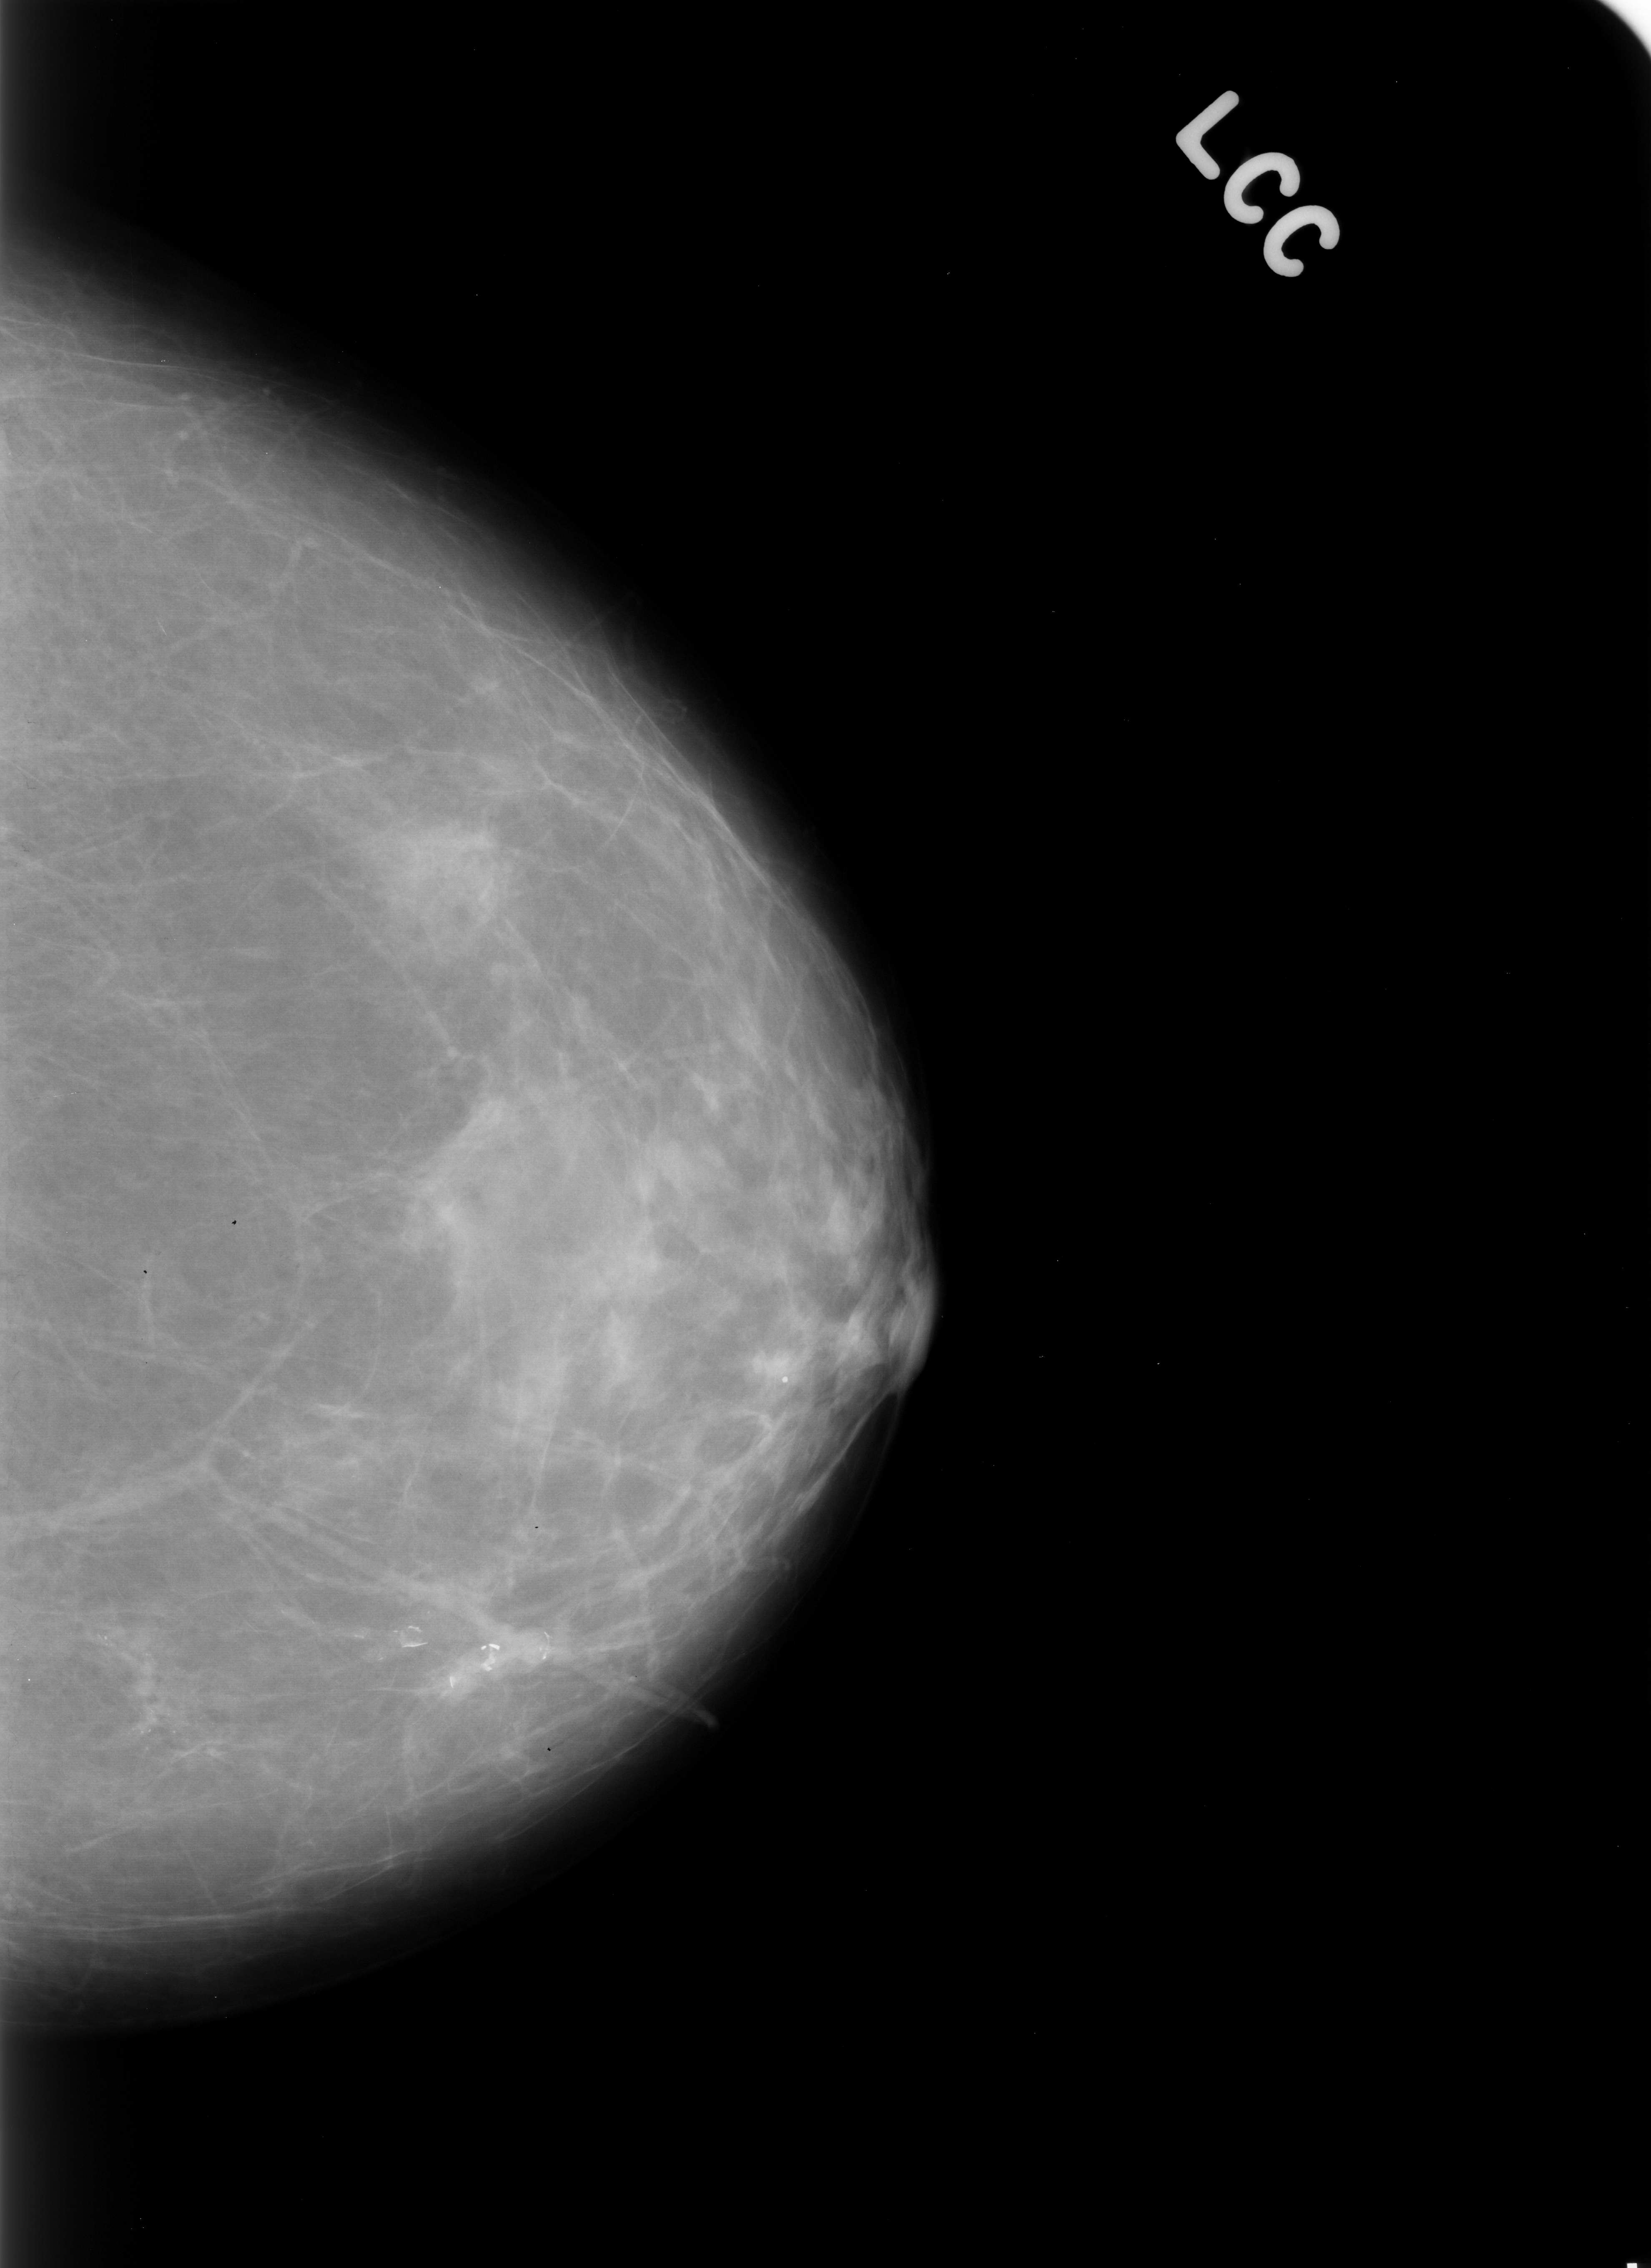
Scanned film-screen mammogram. Left breast. CC view. BI-RADS breast density category 2 (scale 1–4). 1651 × 2268 image matrix.
Expert-marked regions of interest on this film, with their recorded descriptors:
- Finding 1 of 2: calcifications, morphology pleomorphic, distribution clustered; BI-RADS assessment category 4; pathology result (as recorded, not read from the image): malignant: box from (x=33, y=1550) to (x=241, y=1815) px
- Finding 2 of 2: calcifications, morphology eggshell, distribution segmental; BI-RADS assessment category 2; outcome (as recorded, no biopsy): benign without callback (not worked up further): (x=356, y=1577)–(x=581, y=1742)